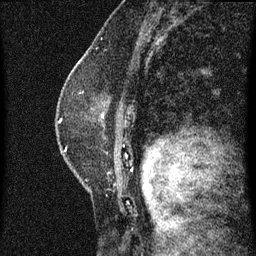
Breast MRI (dynamic contrast-enhanced), one sagittal slice; position 43 of 60 along the scan axis; dynamic contrast-enhanced series, image 2 of 3 at this slice position (ordered by acquisition); 1.5 T; TE 4.2 ms, TR 8 ms; 256 × 256 image matrix, field of view 180 × 180 mm. Female patient, age 47 years.
Annotated regions visible in this slice (semi-automatically segmented with operator editing):
- analysis volume of interest (the breast-tissue region the enhancement analysis was run in; not a lesion): bounding box (x1, y1, x2, y2) in pixels: (56, 80, 133, 187)
- tumour enhancement mask (voxels above the 70 % enhancement threshold inside the analysis volume of interest): (61, 116, 104, 121)